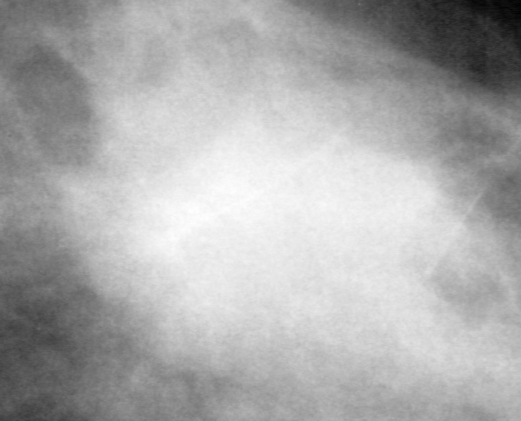
Crop from a digitized film mammogram around one marked abnormality; right breast; CC view; BI-RADS breast density category 3 (scale 1–4).
- Marked abnormality: mass, shape irregular, margins ill defined; BI-RADS assessment category 4; pathology result (as recorded, not read from the image): malignant.